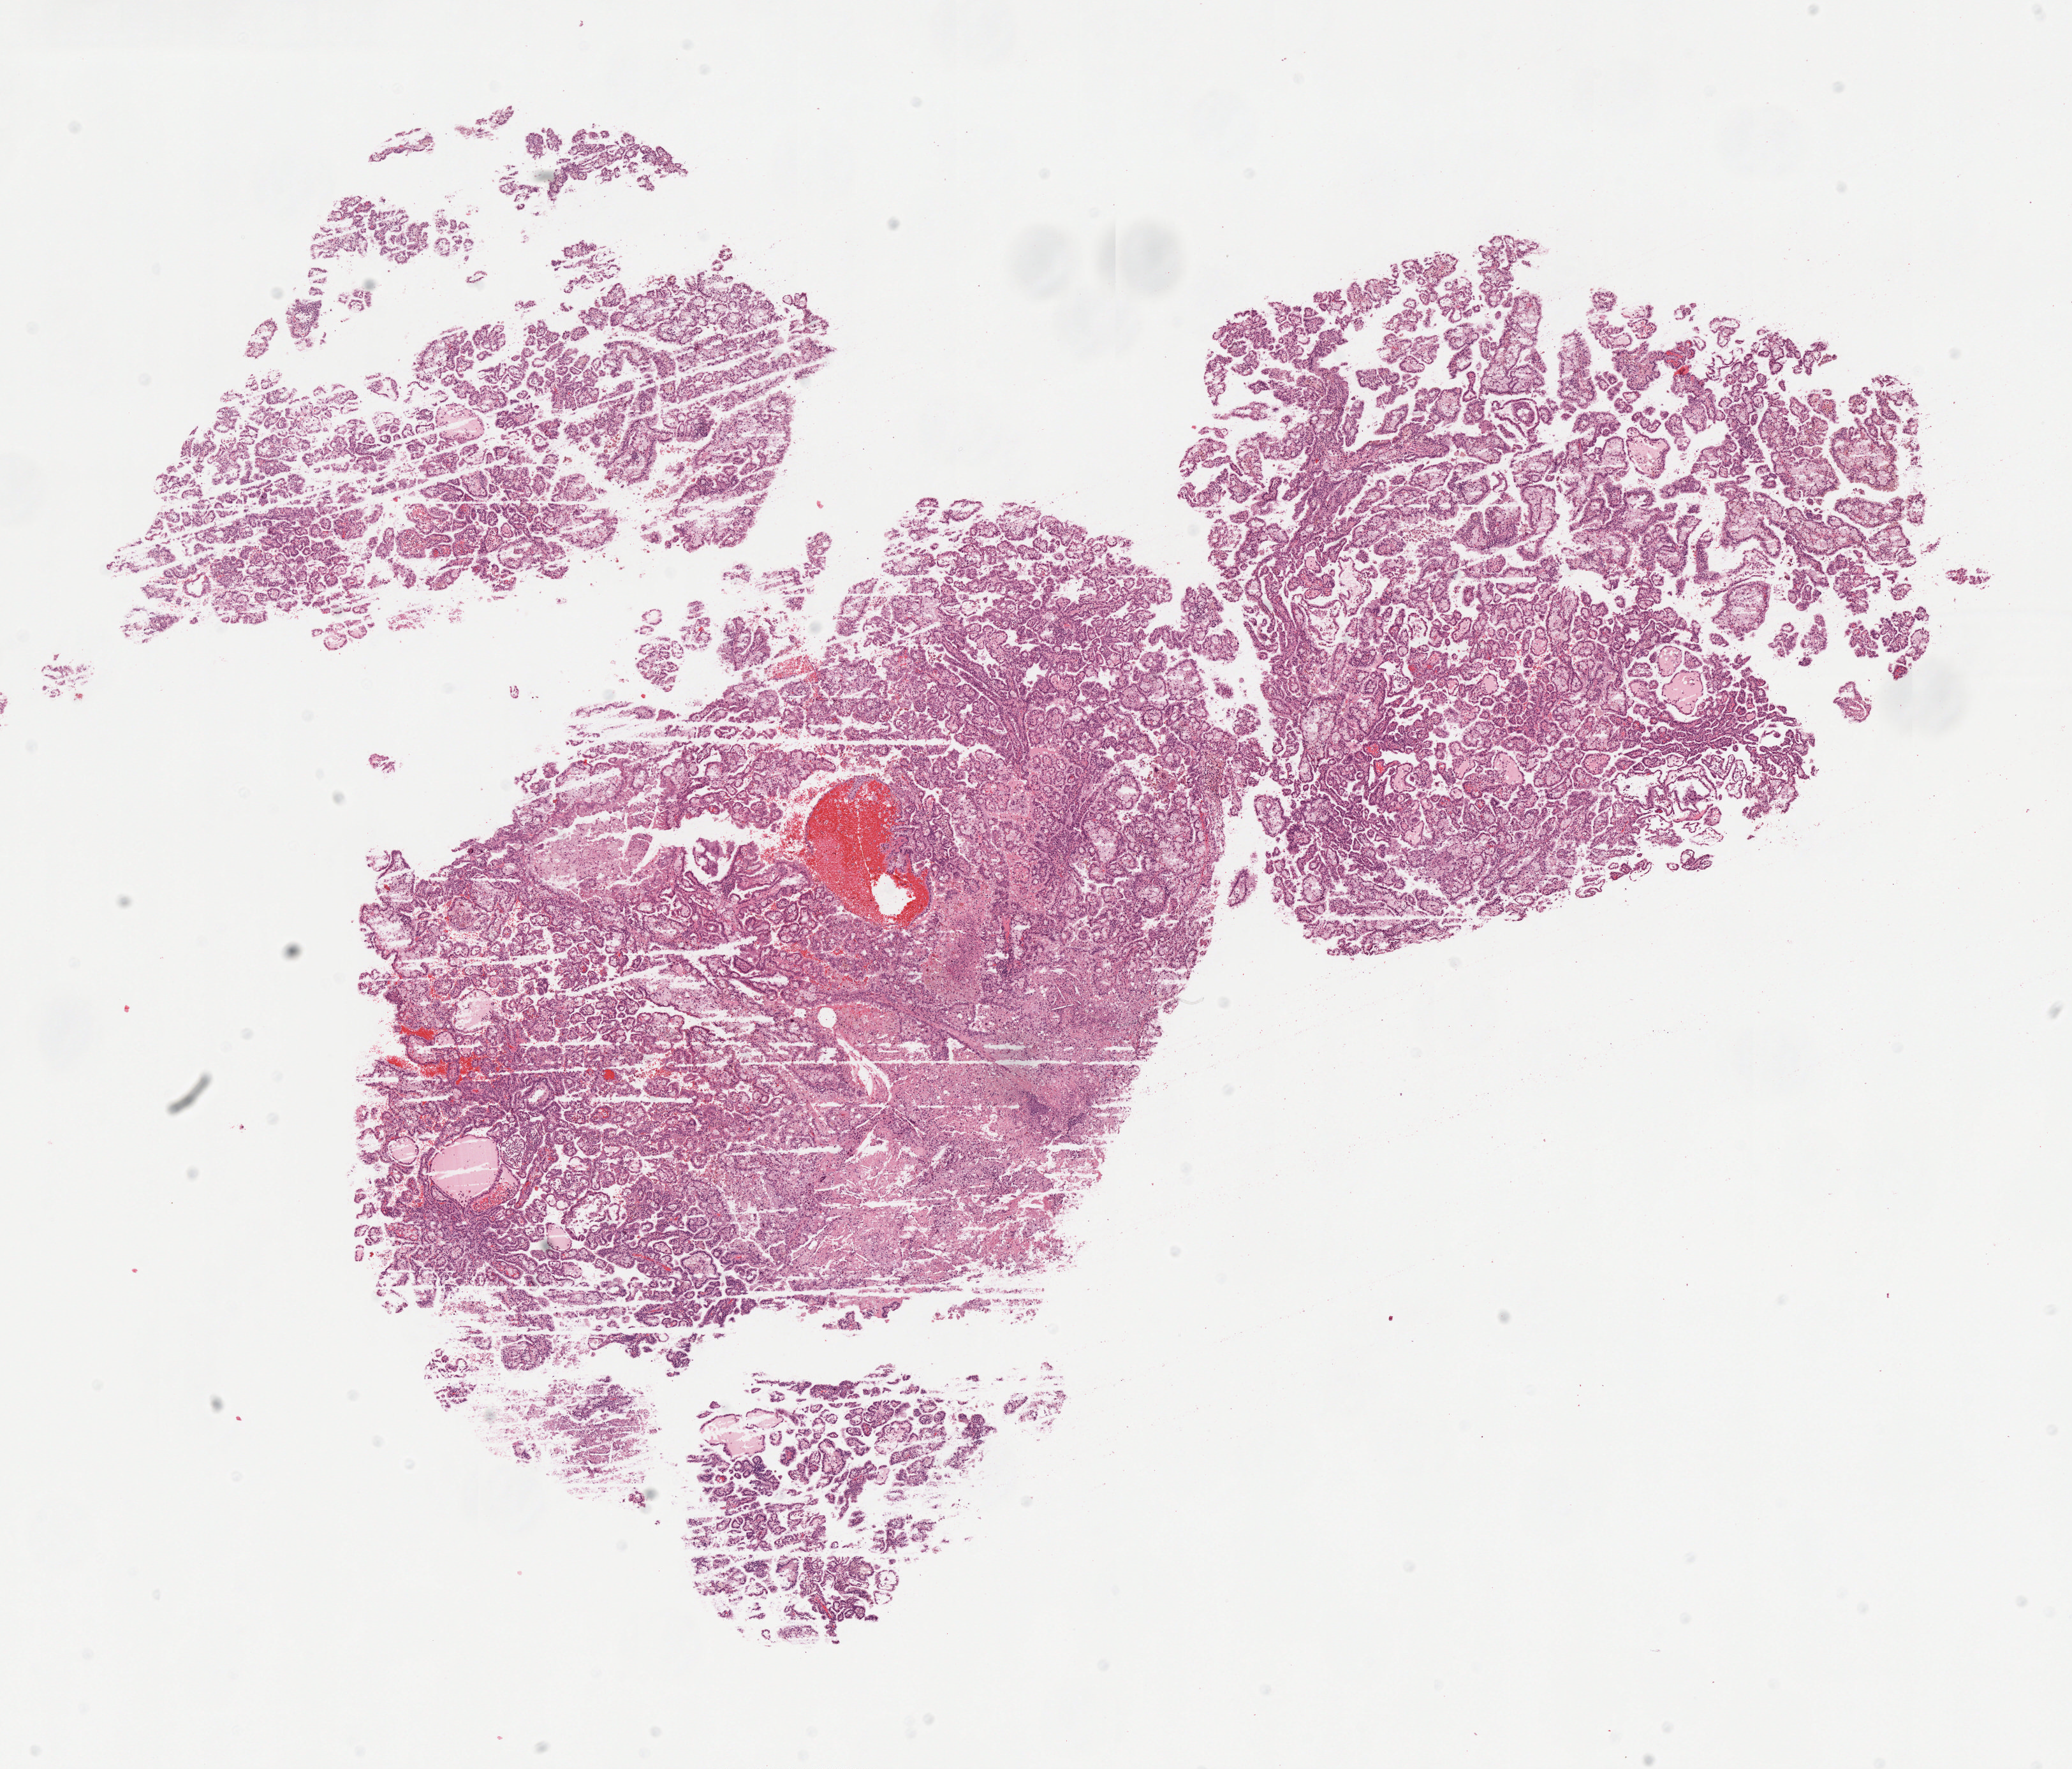
Whole-slide histology image, H&E, shown as a low-resolution overview of the whole scanned area (about 13.0 x 11.1 mm, from a 20x scan); formalin-fixed paraffin-embedded (FFPE) diagnostic section; primary tumour sample from the kidney. Male patient; age at initial diagnosis 51 years.
- diagnosis: Papillary adenocarcinoma, NOS
- AJCC pathologic stage: I (7th edition)